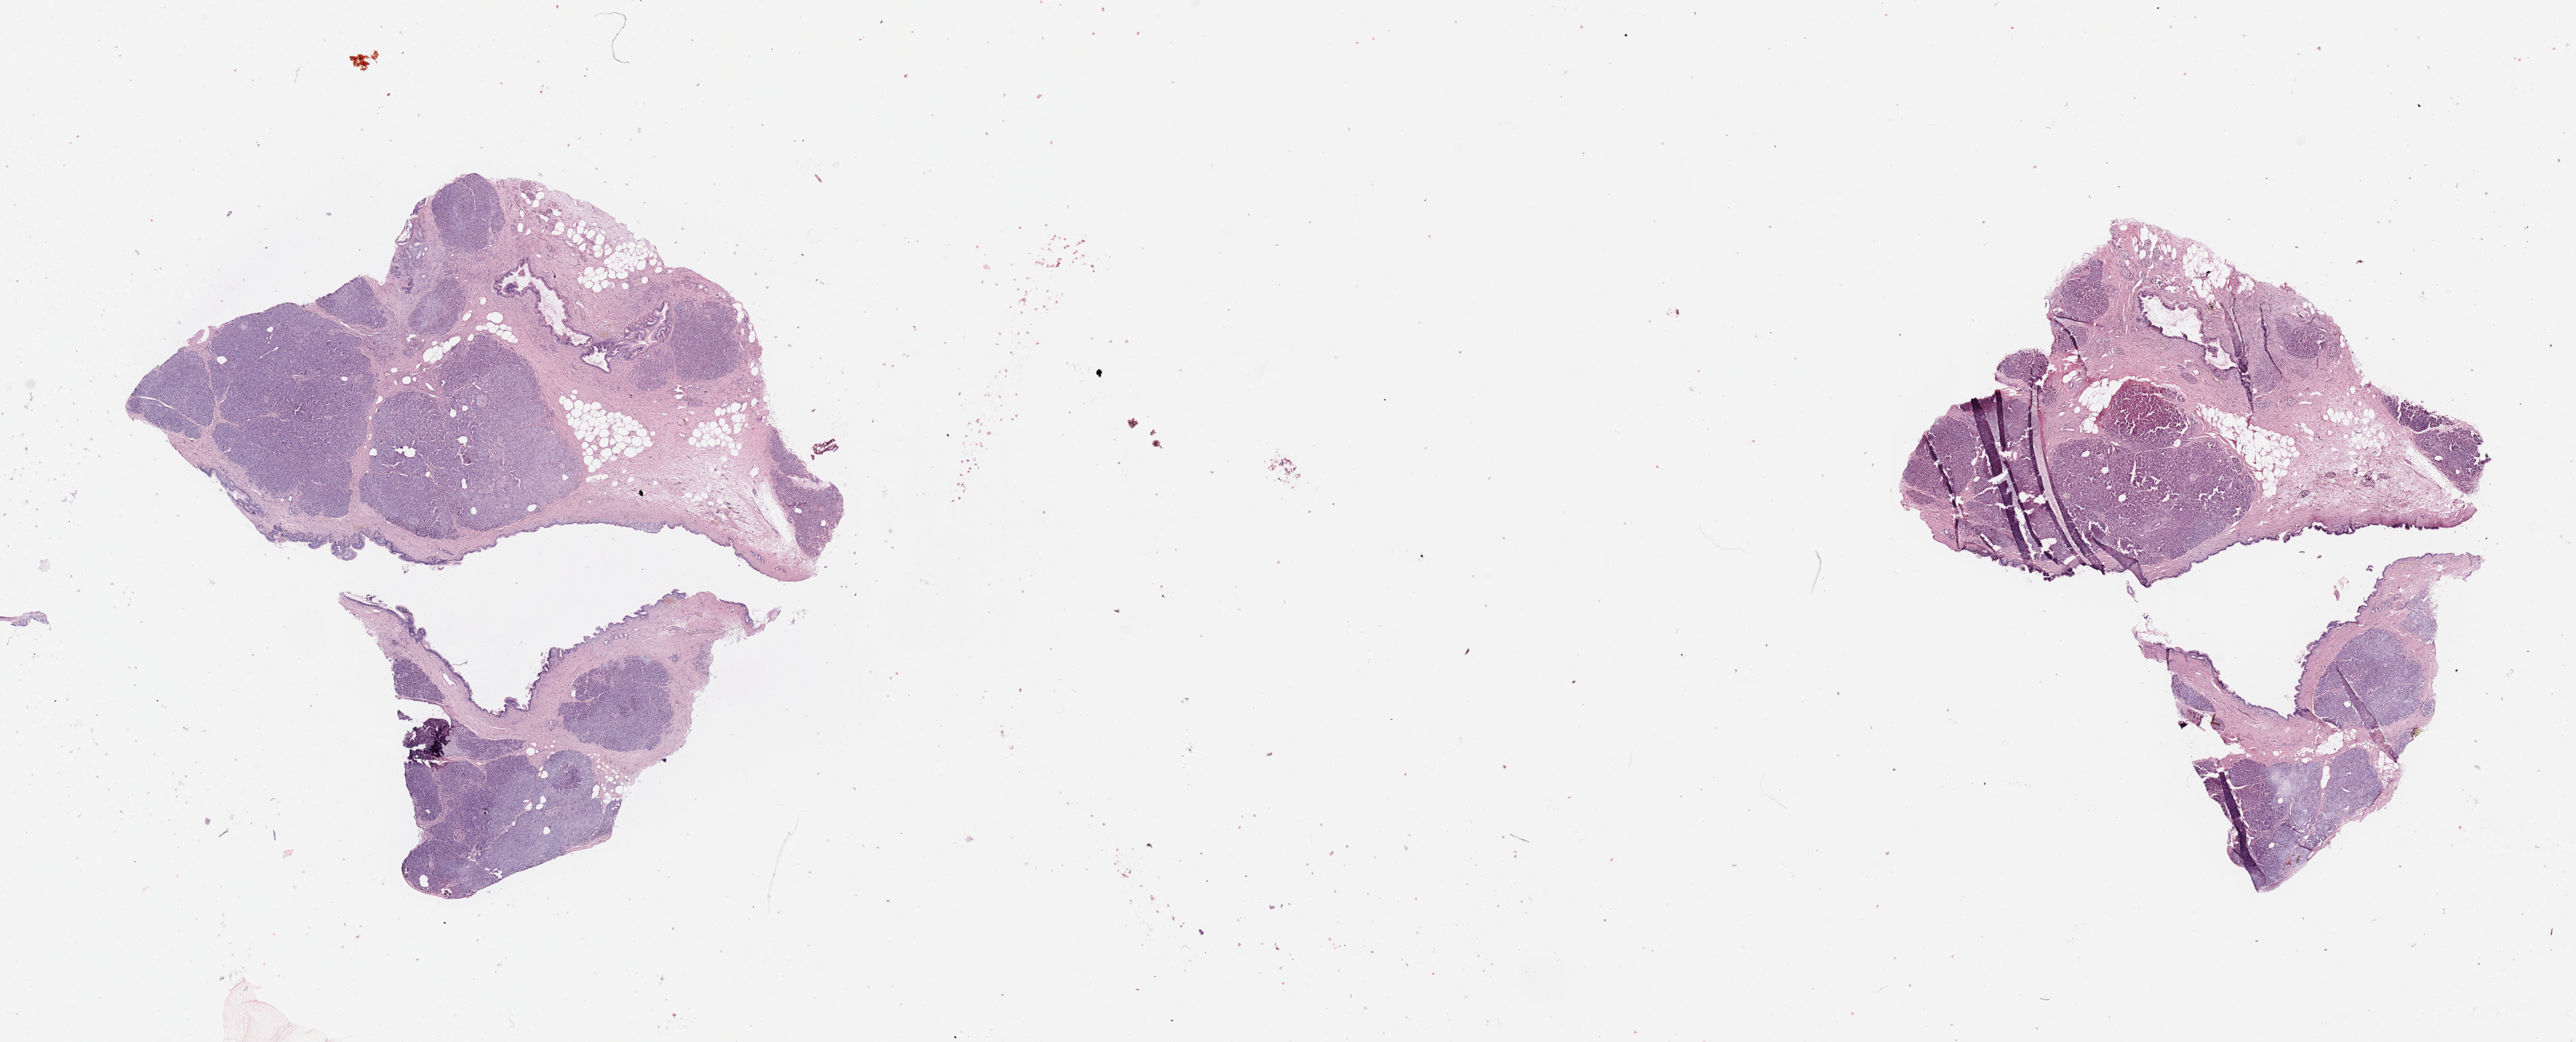
H&E whole-slide image, a low-resolution overview of the entire scanned area, about 29.5 x 12.0 mm. Pancreas, tissue type not recorded.
- patient diagnosis (cohort enrolment): ductal adenocarcinoma (pancreas)